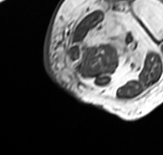
MRI of an extremity soft-tissue mass, one axial slice. Slice 7 of 65 in the series (ordered by position). MR volume resampled by the dataset authors to the PET/CT grid (not the native acquisition matrix). 3.27 mm slice thickness. 163 × 155 image matrix. Female patient. From the clinical record (not read from this slice): histological type: pleomorphic leiomyosarcoma; grade: high; site of the primary tumour: left thigh.
Outlined on this slice (expert contour drawn on MRI and transferred to this co-registered scan by the dataset authors):
- gross tumour volume including surrounding oedema: bounding box [x1, y1, x2, y2] px = [65, 8, 145, 71]